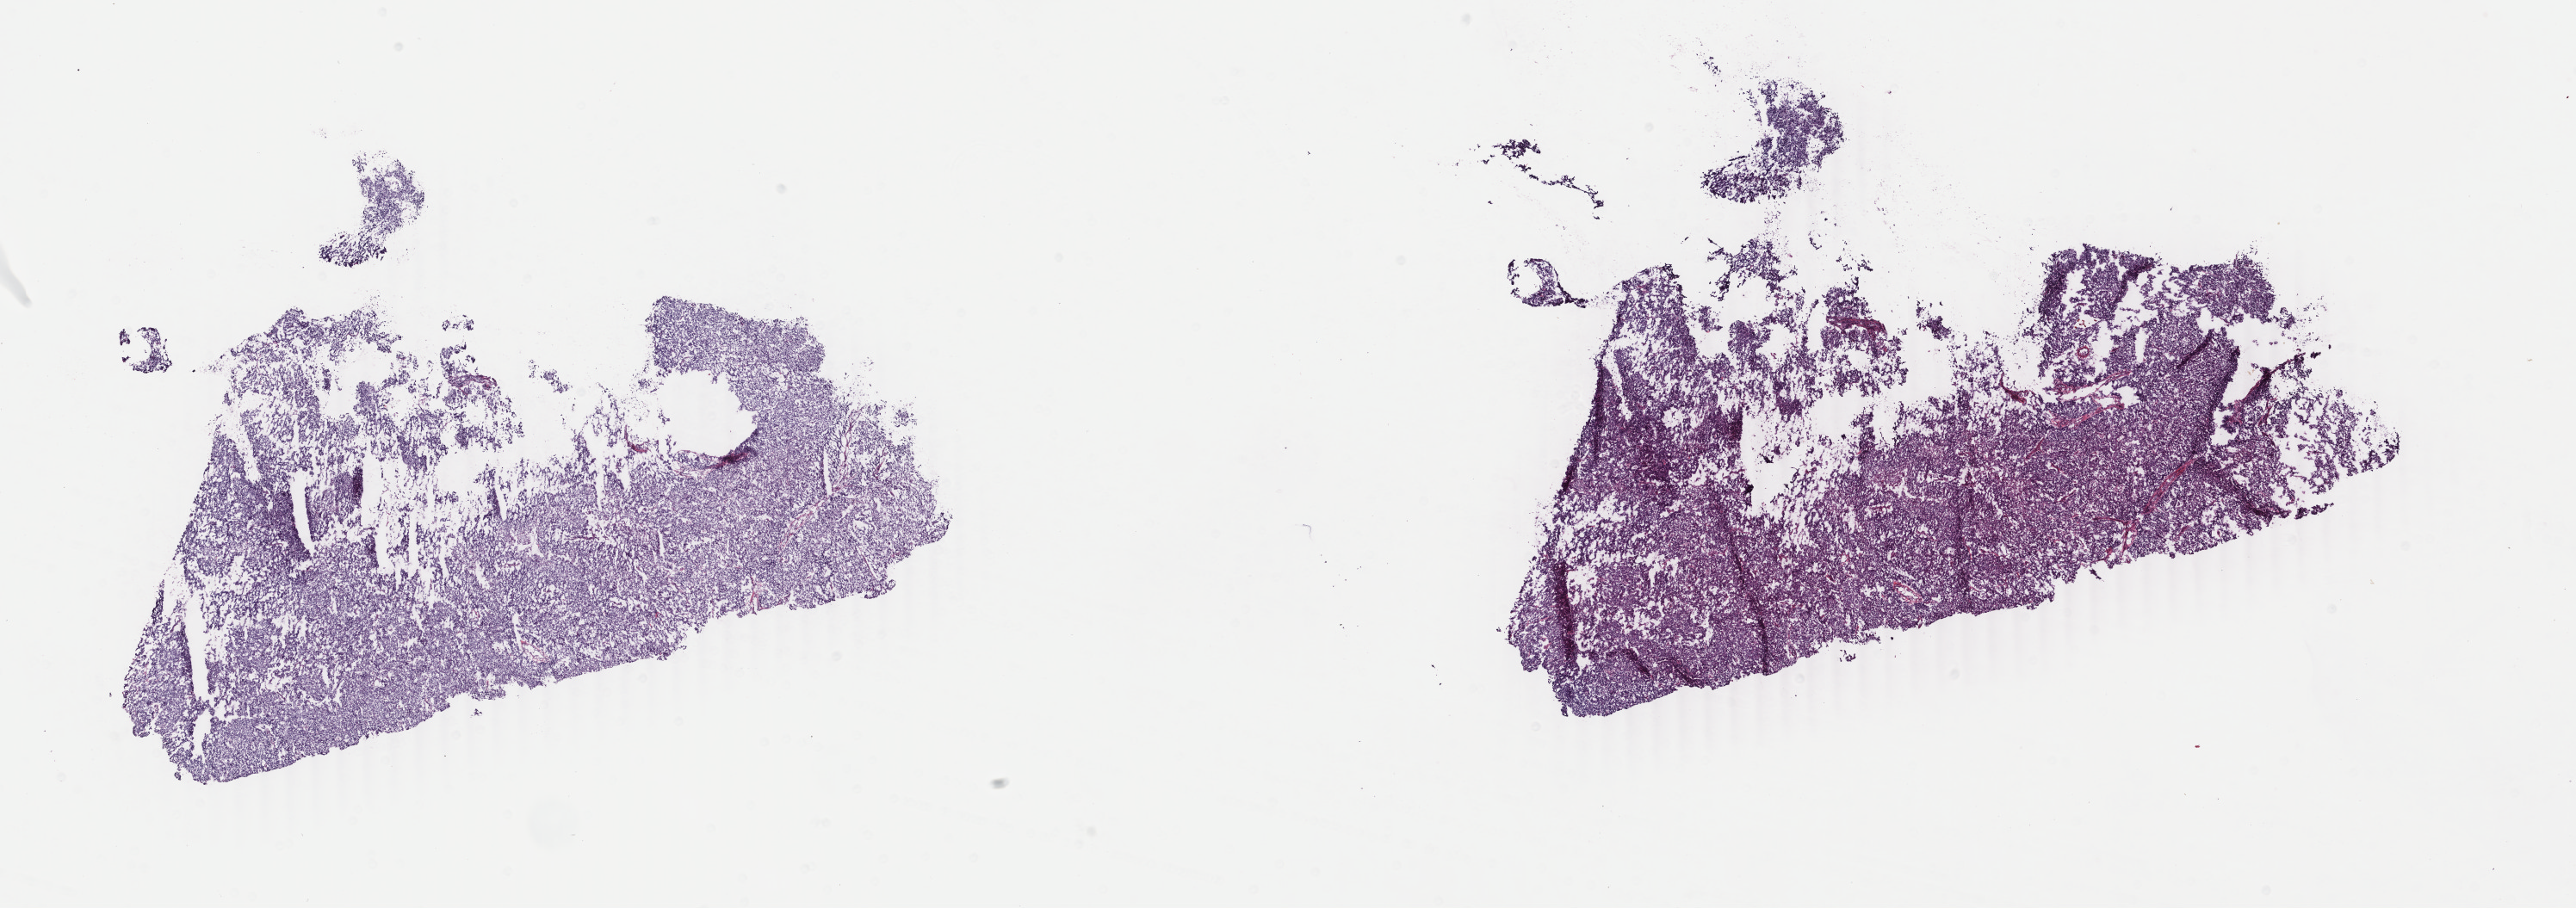
H&E-stained whole-slide image, low-resolution overview of the scanned area, about 23.8 x 8.4 mm. Frozen section. Sample: primary tumour, uterus. Female patient; age at initial diagnosis 68 years. Histologic grade: G2 (moderately differentiated). Slide review estimates, as recorded: tumour cells 100%, tumour nuclei 90%, normal cells 0%, stromal cells 0%, necrosis 0%. Inflammatory infiltration, as recorded: lymphocyte infiltration 0%, monocyte infiltration 0%, neutrophil infiltration 0%.
FIGO stage: IB. Diagnosis: Endometrioid adenocarcinoma, NOS (endometrium).